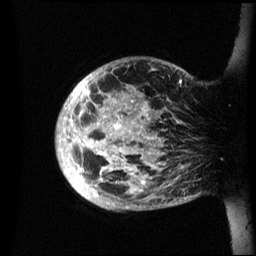
Breast MRI (dynamic contrast-enhanced), one sagittal slice. Slice 9 of 60 in the series (ordered by position). Dynamic contrast-enhanced series, image 2 of 3 at this slice position (ordered by acquisition). 1.5 T. TE 4.2 ms, TR 8.4 ms. 2.4 mm slice thickness. 256 × 256 image matrix. Female patient, age 48 years.
Structures marked on this image (semi-automatic segmentation, software-assisted and operator-edited):
- analysis volume of interest (the breast-tissue region the enhancement analysis was run in; not a lesion): bounding box (x1, y1, x2, y2) in pixels: (56, 57, 201, 211)
- tumour enhancement mask (voxels above the 70 % enhancement threshold inside the analysis volume of interest): (56, 74, 183, 193)